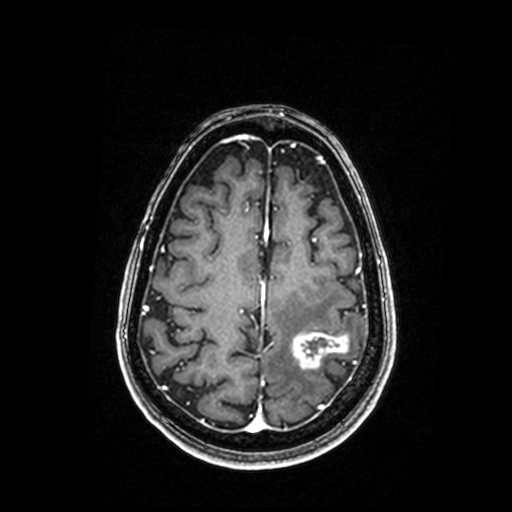
Brain MRI from a brain-tumour surgery series, one axial slice; slice 56 of 192 in the series (ordered by position); T1-weighted post-contrast; 0.98 mm slice thickness; 512 × 512 image matrix. Case-level facts recorded for this patient, not image findings: histopathology: Metastastic Carcinoma, Poorly Differentiated.
Annotated regions visible in this slice (manually delineated by an expert):
- tumour: bounding box (x1, y1, x2, y2) in pixels: (293, 332, 348, 368)